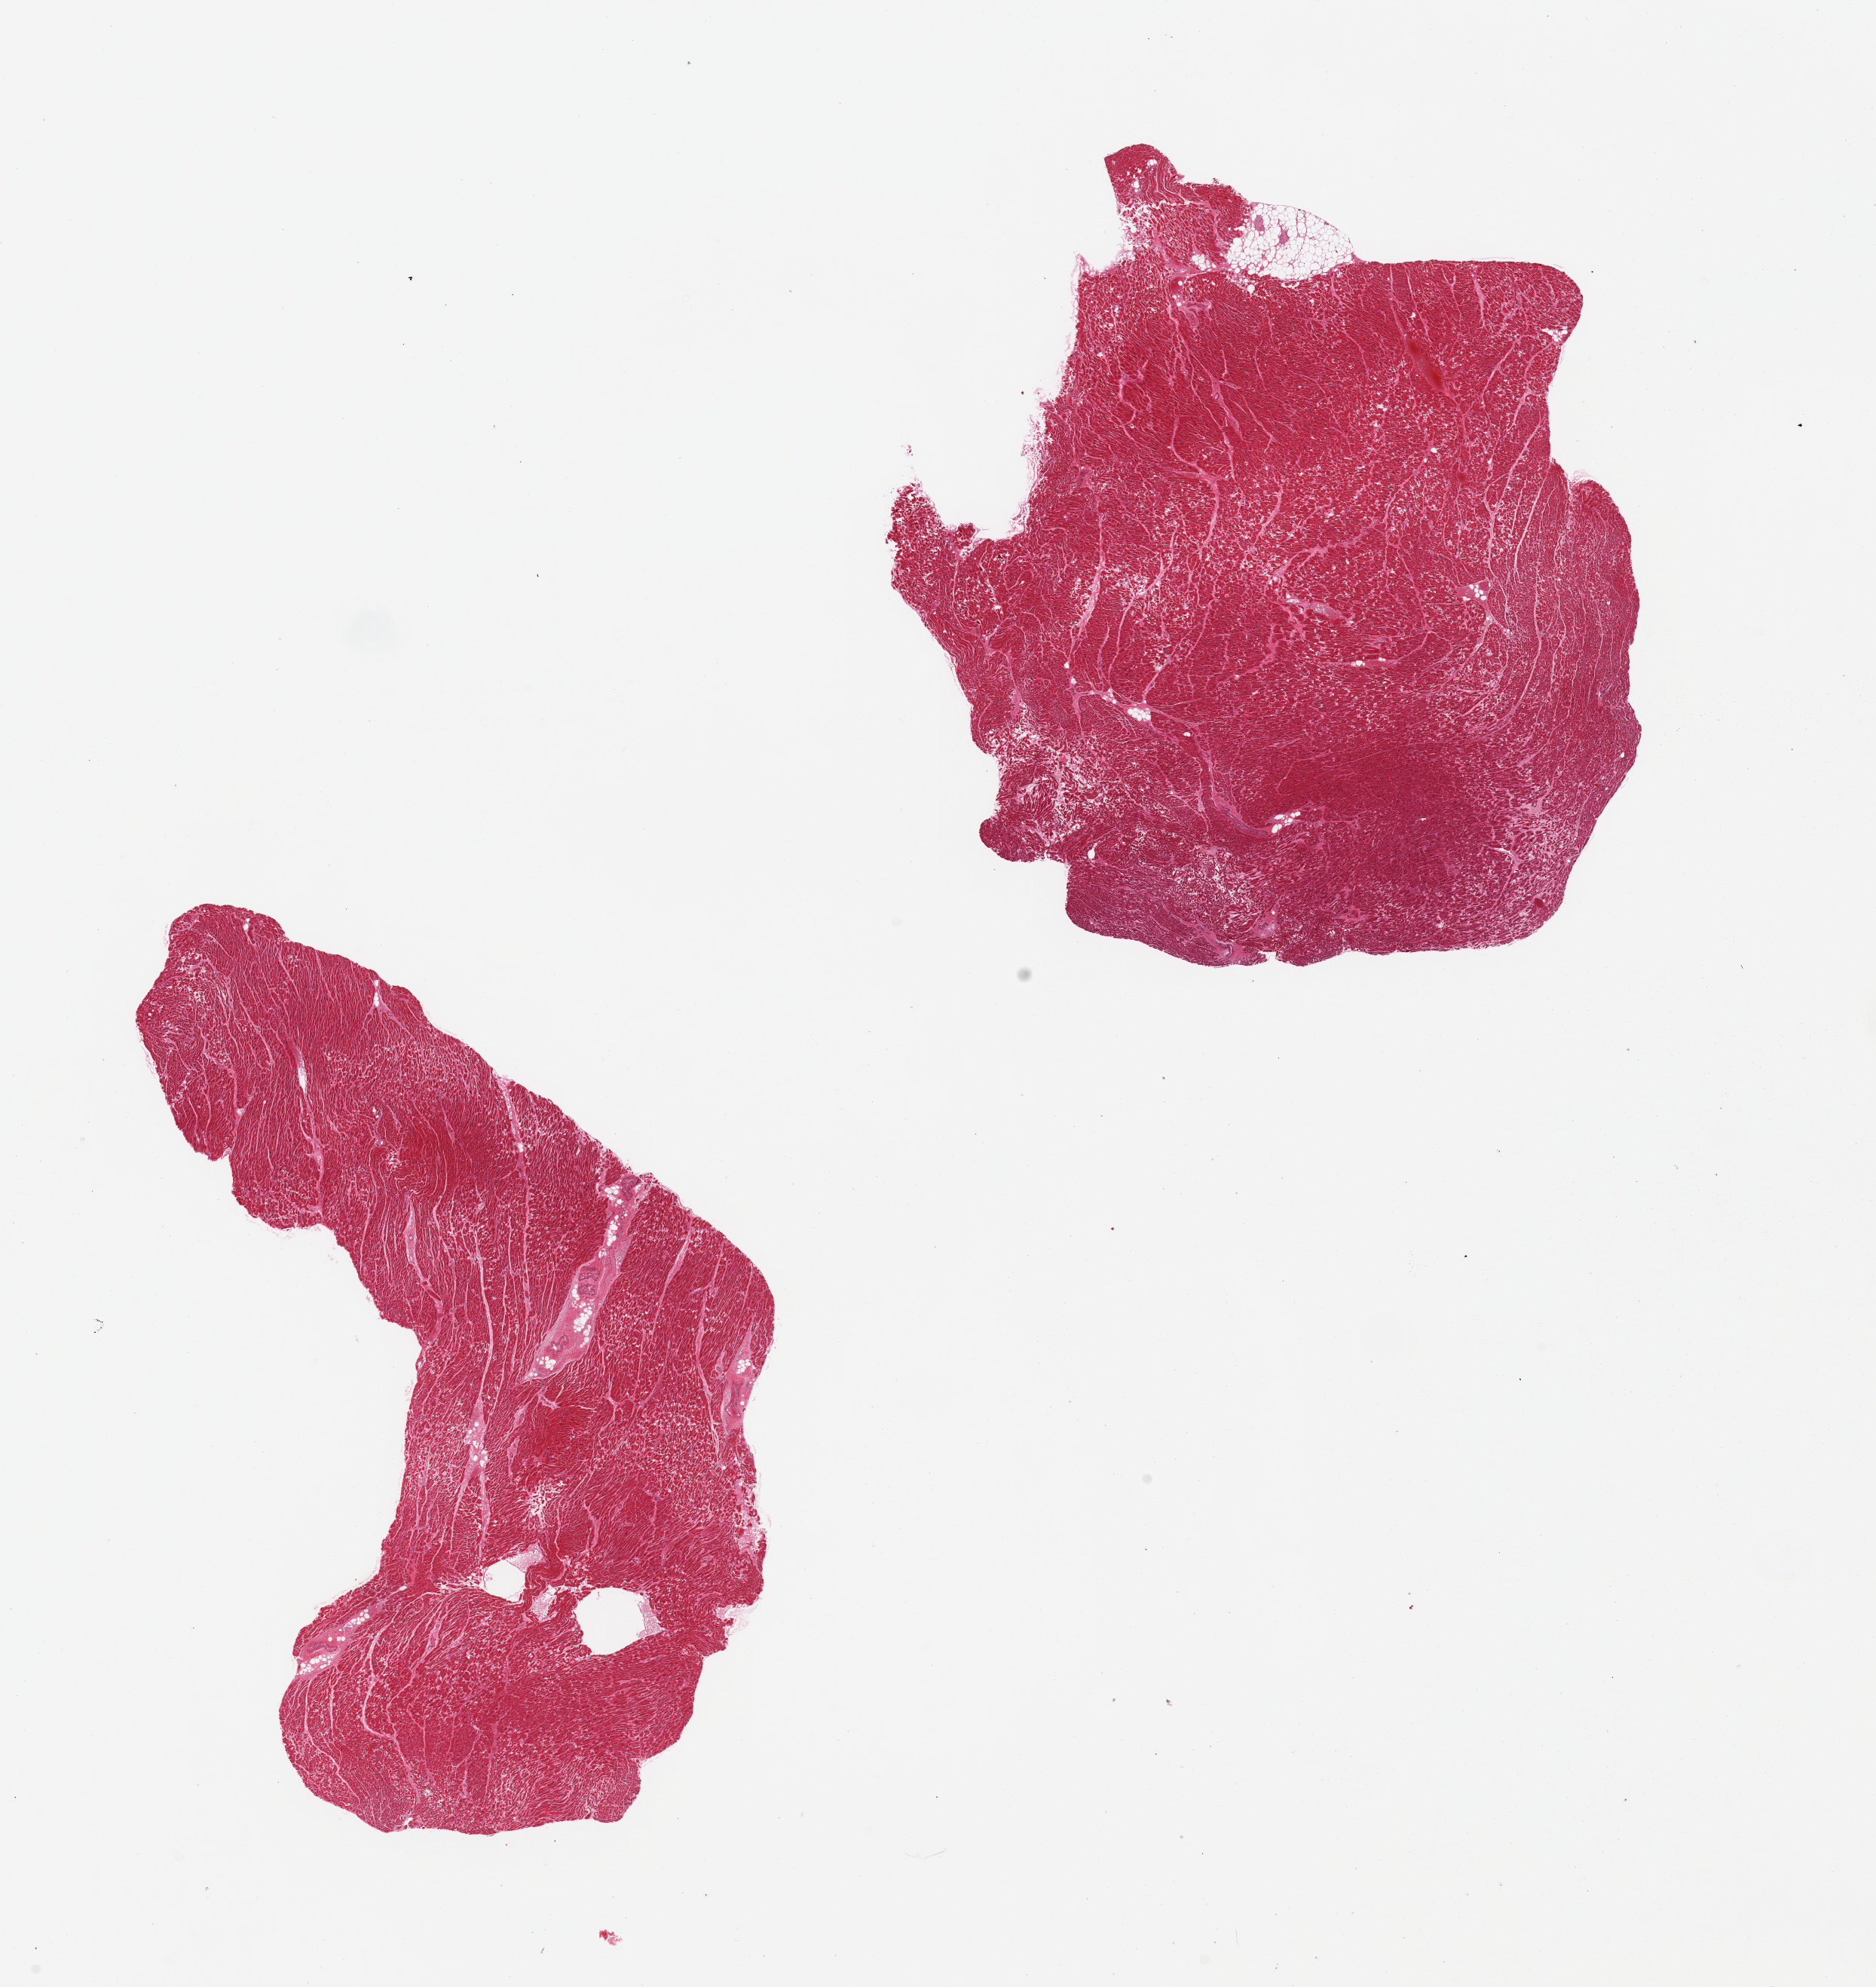
Haematoxylin and eosin whole-slide image — low-resolution overview of the scanned area, about 19.7 x 20.9 mm. PAXgene-fixed, paraffin-embedded tissue. Section of heart (target tissue). Tissue donor sample. Male donor.
* reviewer comment on this tissue sample: 2 pieces. Possible early ischemia and hypertrophy